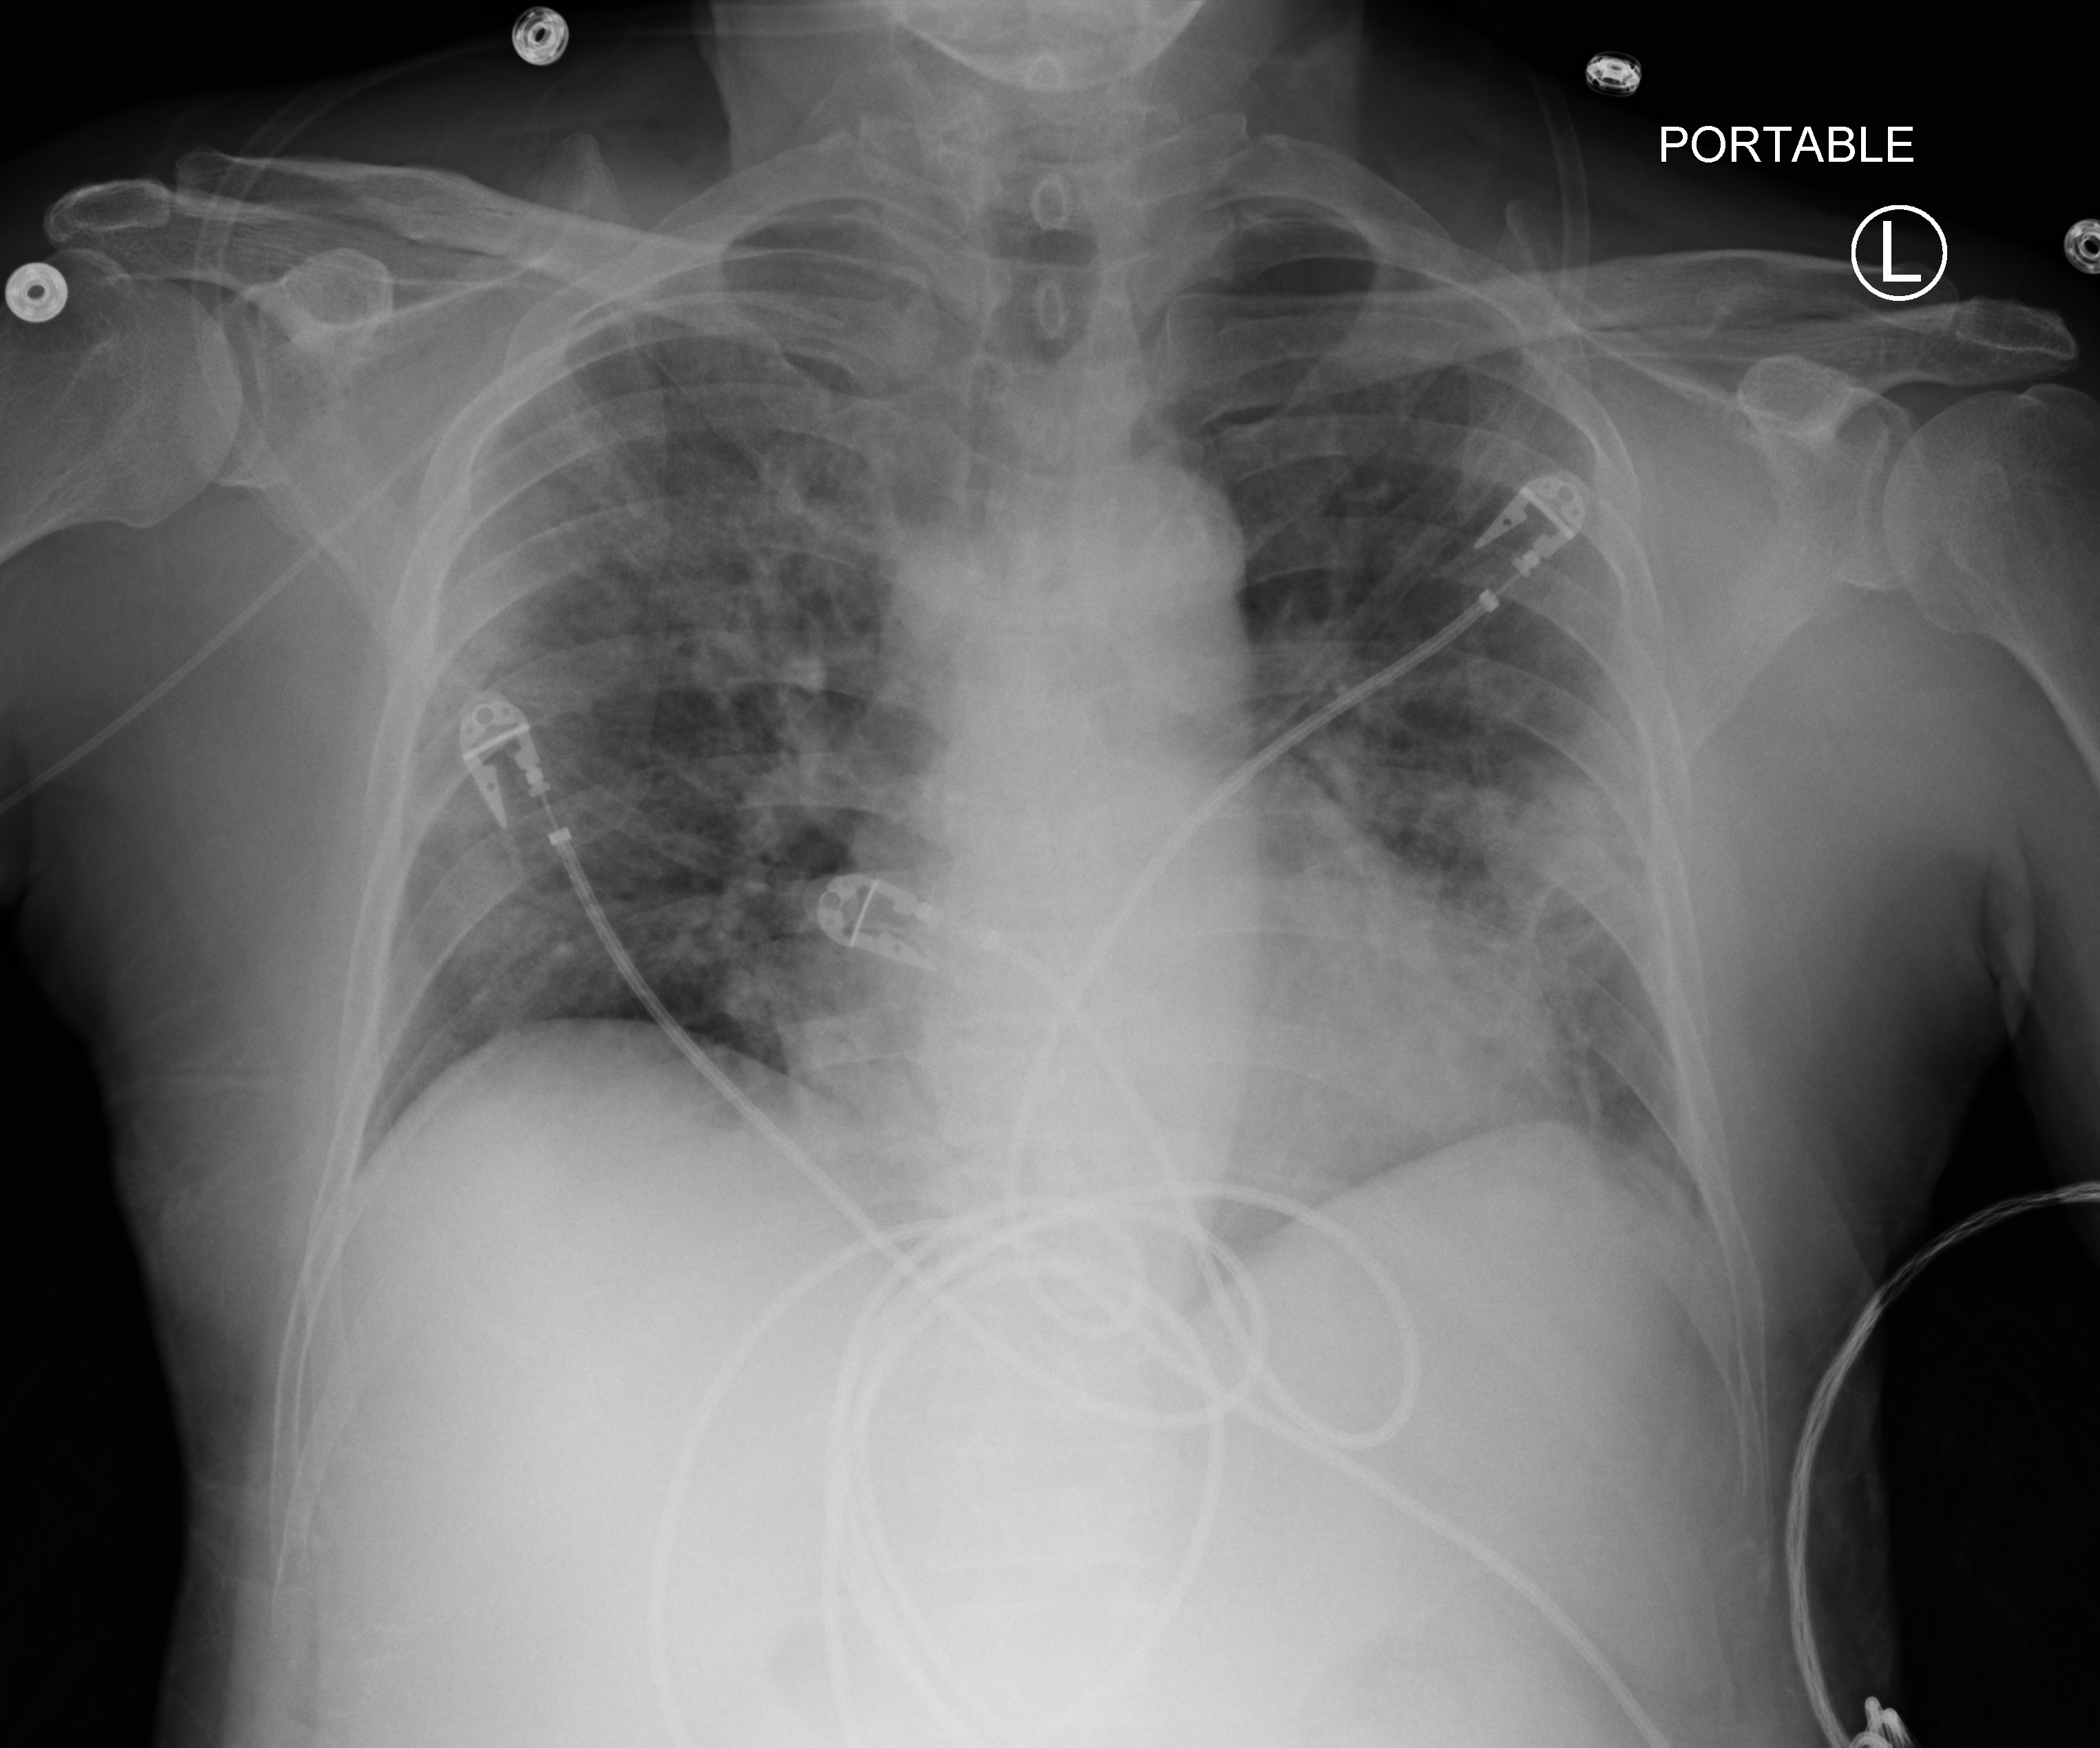
Chest X-ray (portable); anteroposterior (AP) projection. Patient hospitalised with COVID-19; male, aged 60–74 years.
Admission-level facts for this patient (not findings on this image; timing relative to this image not recorded): admitted to intensive care during this hospital stay: no.